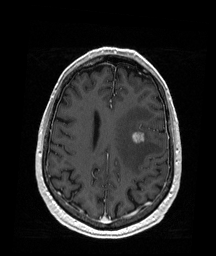
Brain MRI from a brain-tumour surgery series, one axial slice. Slice 66 of 176 in the series (ordered by position). T1-weighted post-contrast. 1 mm slice thickness. 216 × 256 image matrix, field of view 211 × 250 mm. From the clinical record (not read from this slice): histopathology: Metastatic Melanoma.
Outlined on this slice (expert manual segmentation):
- tumour: box from (x=132, y=132) to (x=145, y=143) px